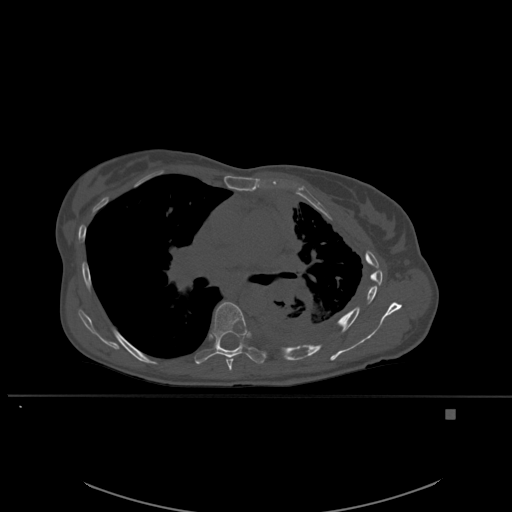
CT including the spine, one axial slice. Position 370 of 537 along the scan axis. Bone window (W 1800 / L 400 HU). 512 × 512 image matrix, field of view 440 × 440 mm. Patient: female, 45 years. Case-level facts recorded for this patient, not image findings: primary cancer: lung.
Annotated regions visible in this slice (semi-automatically segmented with operator editing):
- T6 vertebra: bounding box [x1, y1, x2, y2] px = [226, 357, 233, 371]
- T7 vertebra: [196, 302, 266, 365]